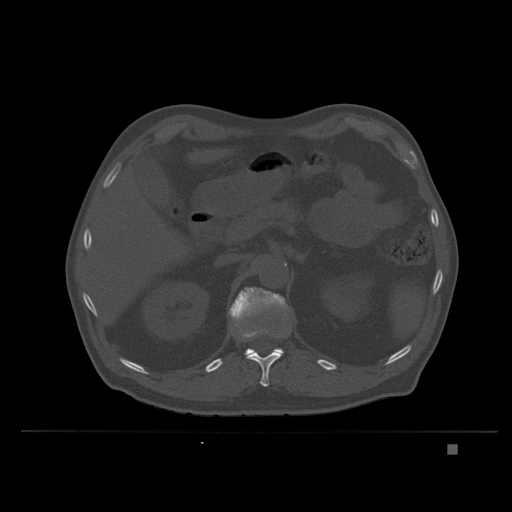
CT including the spine, one axial slice. Position 151 of 435 along the scan axis. Bone window (W 1800 / L 400 HU). 512 × 512 image matrix, field of view 434 × 434 mm. Male patient, age 73 years. From the clinical record (not read from this slice): primary cancer: skin.
Outlined on this slice (semi-automatically segmented with operator editing):
- L1 vertebra: bounding box [x1, y1, x2, y2] px = [229, 287, 289, 384]
- T12 vertebra: [247, 326, 292, 387]